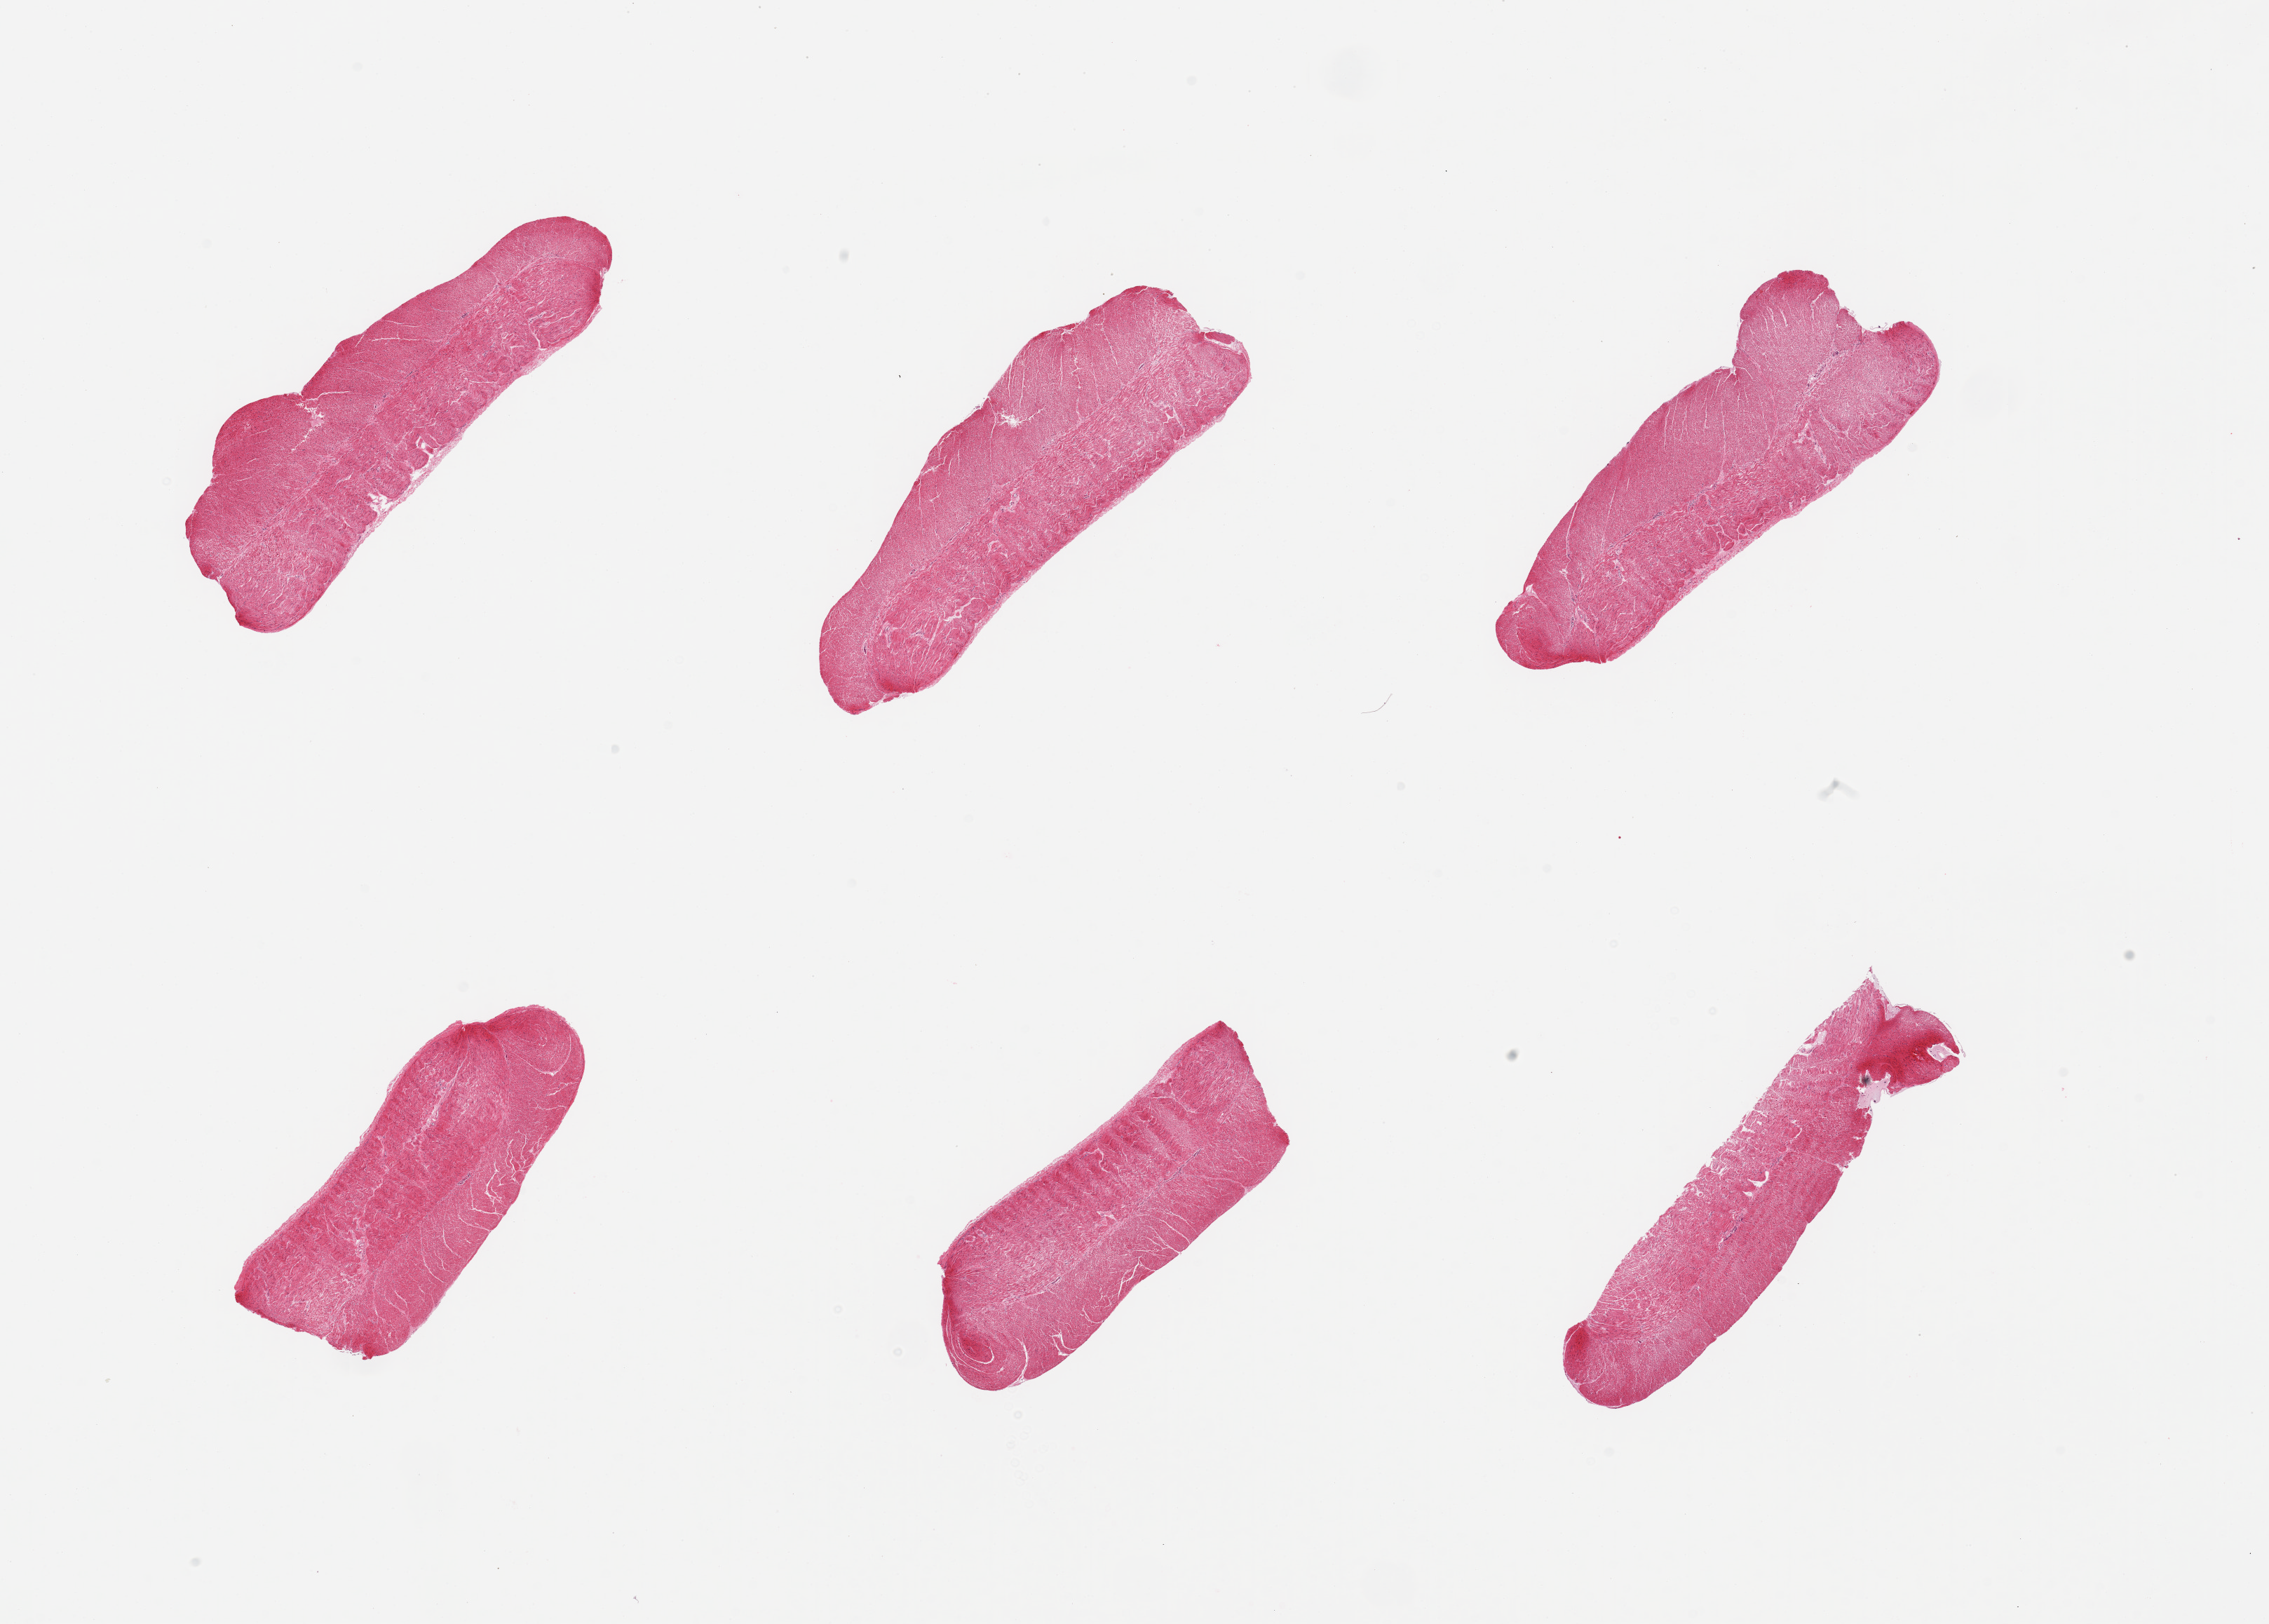
Haematoxylin and eosin whole-slide image — a low-resolution overview of the entire scanned area, about 25.6 x 18.3 mm. PAXgene-fixed, paraffin-embedded tissue. Sampled site (target tissue): sigmoid colon. Tissue donor sample. Male donor.
Reviewer comment on this tissue sample: 6 pieces, all target muscularis, good specimens.